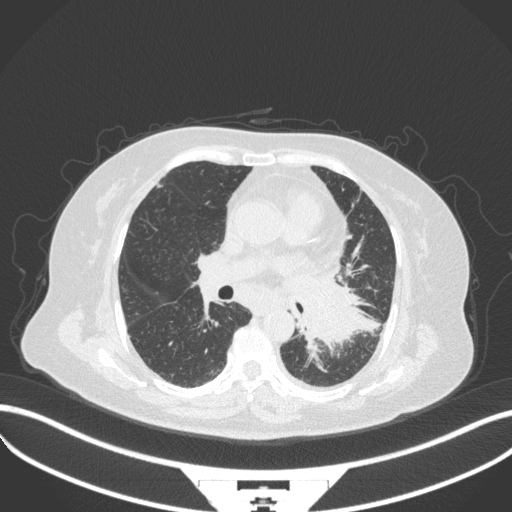
Chest CT, one axial slice; position 187 of 328 along the scan axis; 120 kVp; lung window (W 1500 / L -600 HU); 1 mm slice thickness; 512 × 512 image matrix, field of view 400 × 400 mm. Female patient, age 69 years. Case-level facts recorded for this patient, not image findings: clinical TNM (as recorded): T2b N3 M1.
Structures marked on this image (rectangle marked by the reading radiologist):
- lung tumour (recorded histology: adenocarcinoma): bounding box <294,279,379,355> (left, top, right, bottom; pixels)